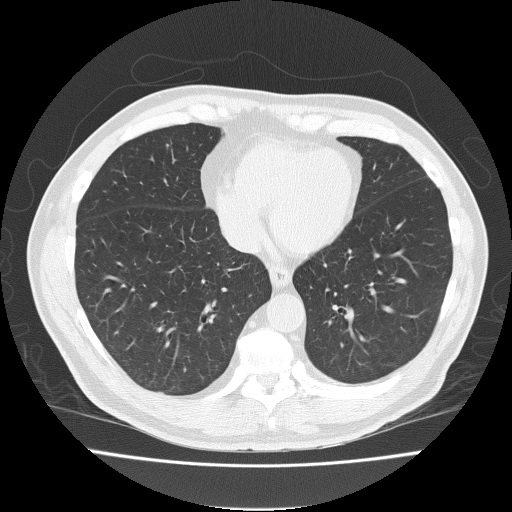
Chest CT (low-dose screening protocol), one axial image. Baseline screening round. Lung window (W 1500 / L -600 HU). 2 mm slice thickness. Slice 130 of 191 in the series. 512 × 512 image matrix, field of view 375 × 375 mm. Male, age 57 years at enrolment.
• Expert reader's lesion annotation, box from (x=145, y=135) to (x=184, y=158) px.
• Reader record for this screening exam (exam-level; its link to the box is not recorded): non-calcified nodule or mass ≥4 mm, right middle lobe, 4 × 4 mm, spiculated (stellate) margins, soft tissue attenuation.
• Participant outcome: lung cancer diagnosed 459 days after this screen — adenocarcinoma, NOS, right middle lobe, moderately differentiated (G2), stage IA (AJCC 6th edition), 12 mm at pathology.